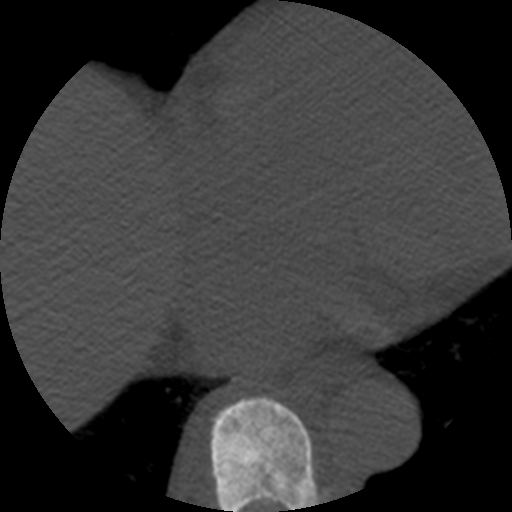
CT including the spine, one axial slice. Position 310 of 508 along the scan axis. 120 kVp. Bone window (W 1800 / L 400 HU). 1.25 mm slice thickness. 512 × 512 image matrix, field of view 160 × 160 mm. Patient age 57 years. Case-level facts recorded for this patient, not image findings: primary cancer: prostate.
Annotated regions visible in this slice (semi-automatic segmentation, software-assisted and operator-edited):
- T8 vertebra: bounding box (x1, y1, x2, y2) in pixels: (210, 397, 327, 512)